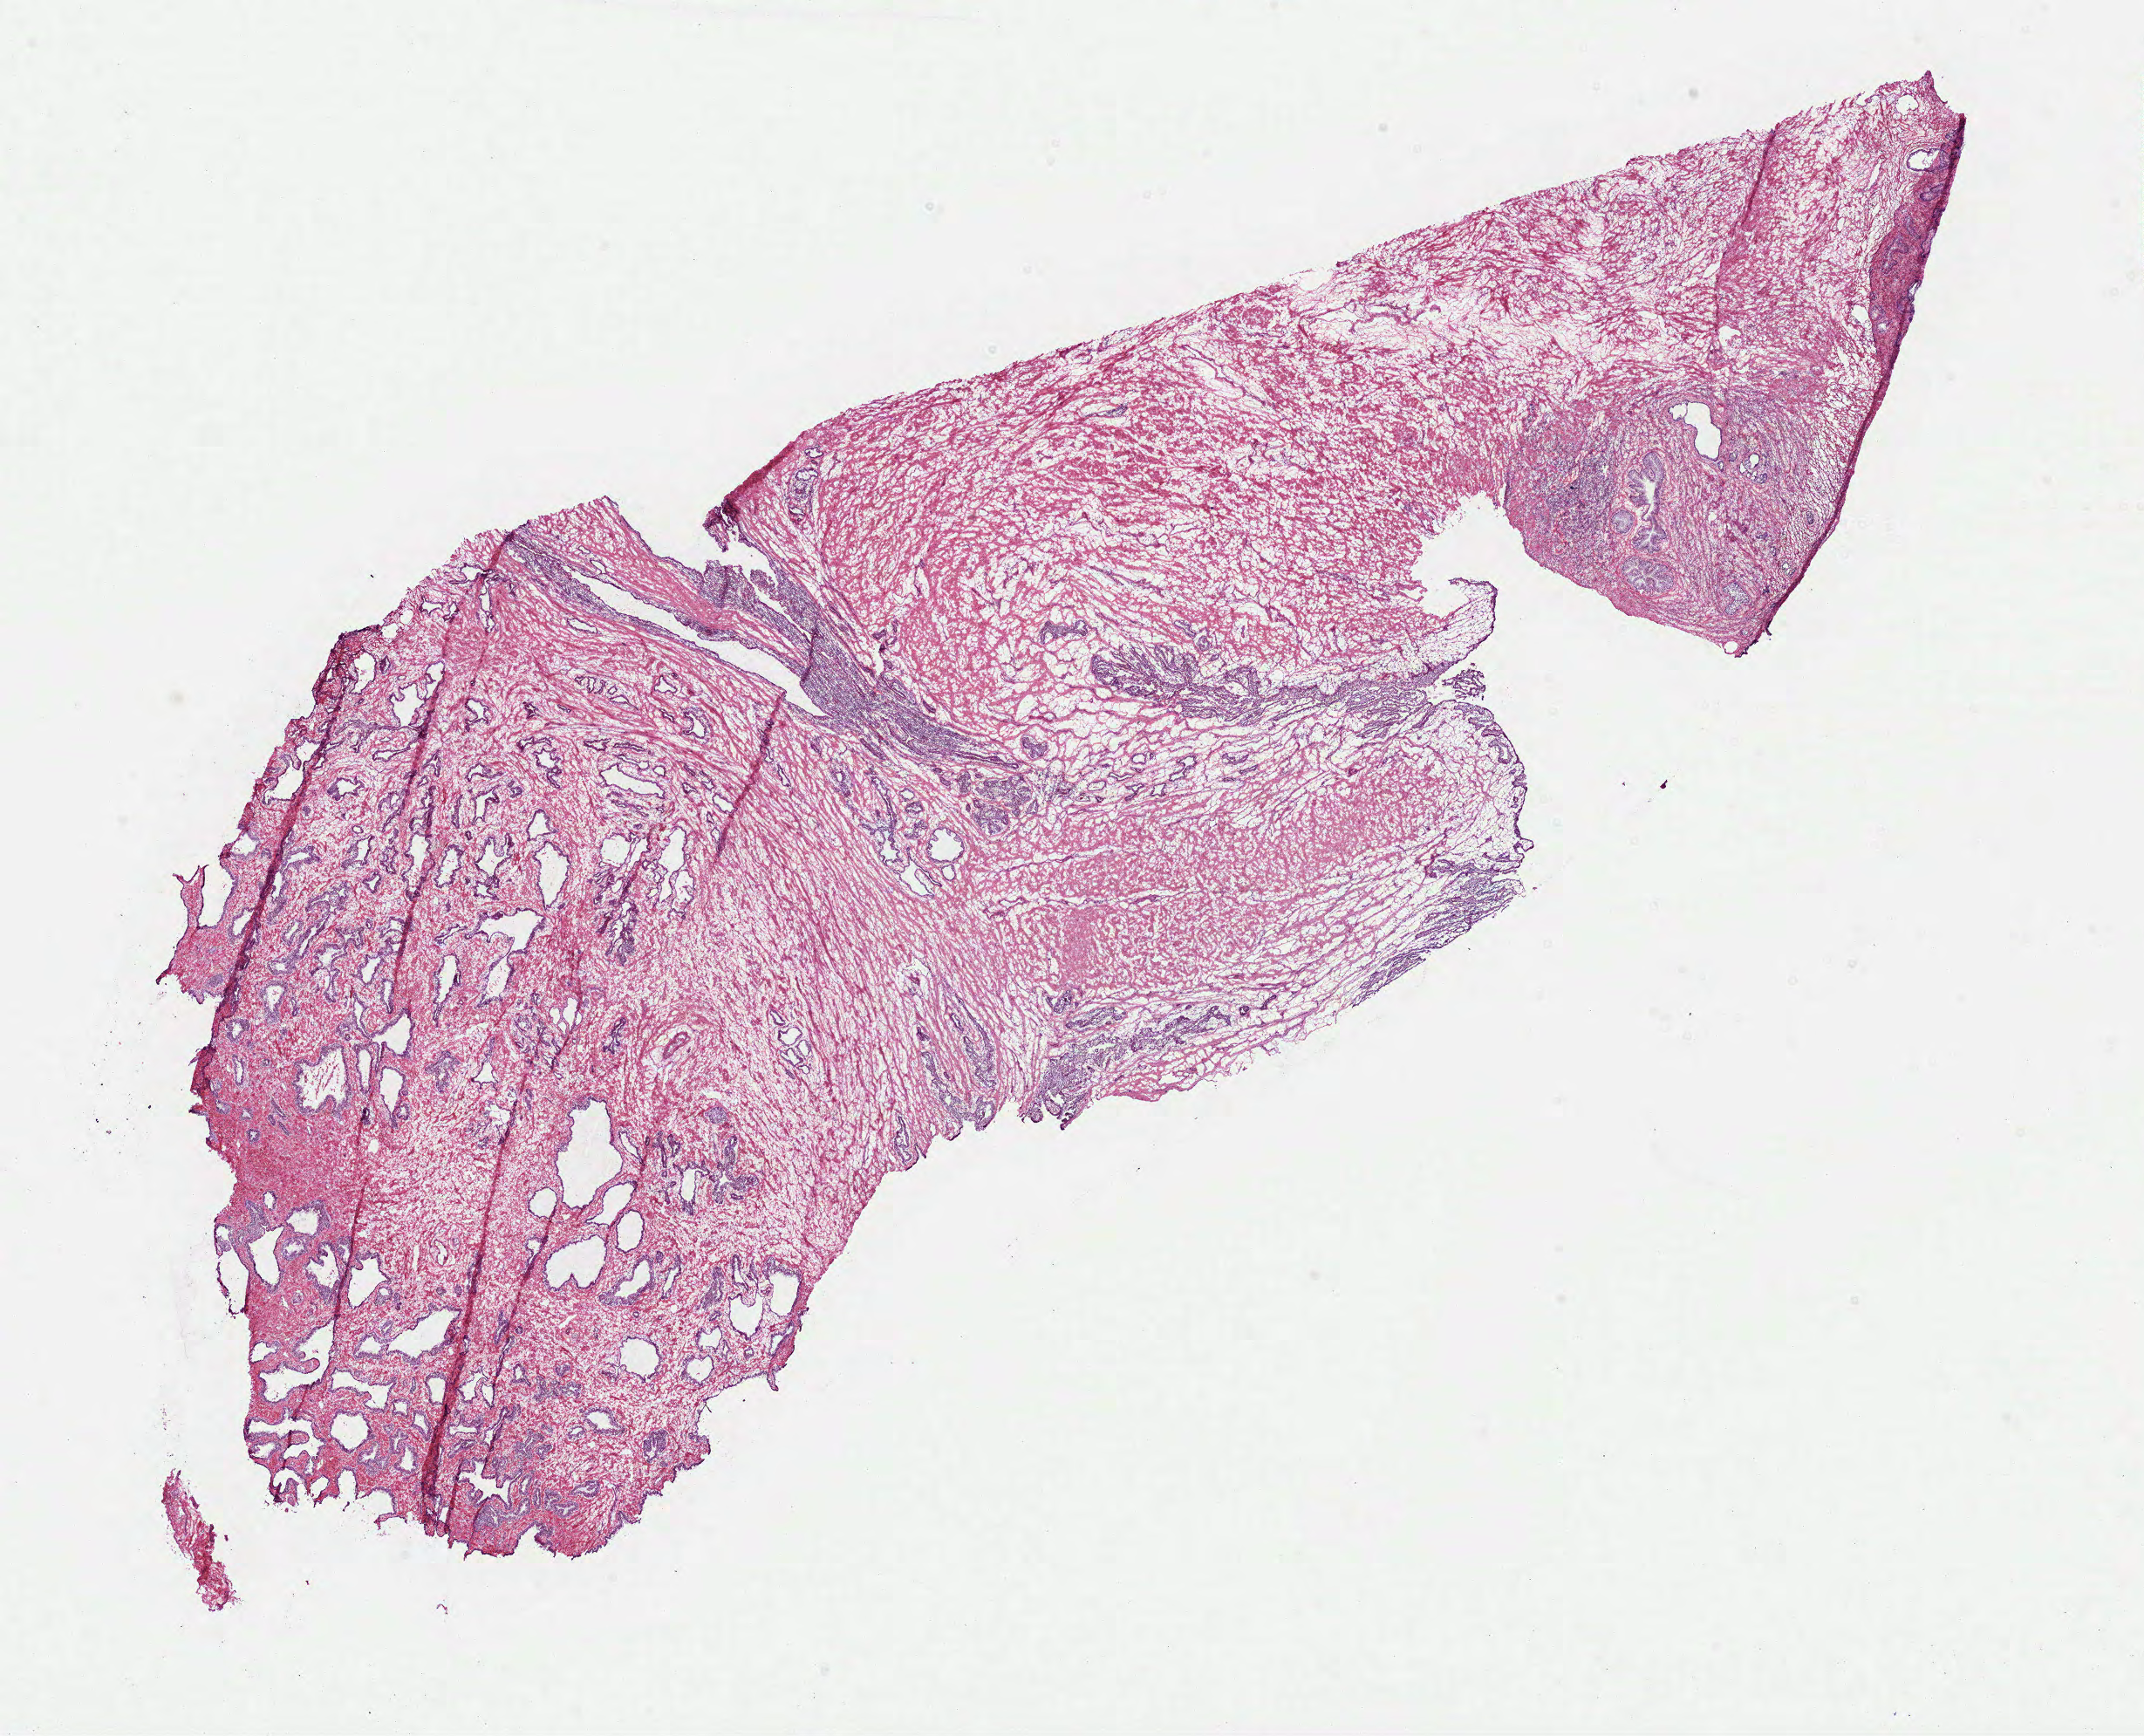
Hematoxylin and eosin (H&E) stained whole-slide image — whole scanned area (about 19.8 x 16.0 mm, acquisition: 40x scan) shown as a low-resolution overview, frozen section, sample: solid tissue normal (non-tumour tissue), prostate. Male, age 71 years at initial diagnosis.
- this section: solid tissue normal (non-tumour) sample from the same patient
- patient diagnosis: Acinar cell carcinoma (prostate gland)